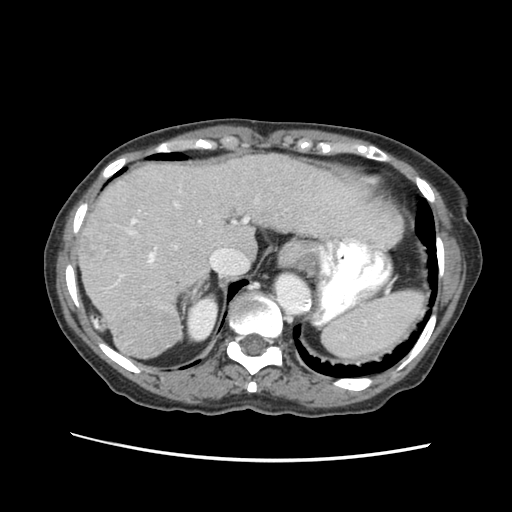
Contrast-enhanced abdominal CT (liver protocol), one axial slice. Slice 44 of 63 in the series (ordered by position). Reconstruction kernel STANDARD. Soft-tissue window (W 400 / L 40 HU). 512 × 512 image matrix, field of view 340 × 340 mm. Case-level facts recorded for this patient, not image findings: diagnosis: hepatocellular carcinoma (patient treated with transarterial chemoembolisation; whether this scan precedes or follows treatment is not stated here); TNM stage (as recorded): Stage-I; Child-Pugh class: B; tumour differentiation: well differentiated.
Outlined on this slice (semi-automatically segmented with operator editing):
- liver parenchyma outside the tumour (the mass and vessels are separate outlines, so this box may not span the whole liver): bounding box [x1, y1, x2, y2] px = [76, 150, 402, 358]
- mass: [113, 302, 179, 357]
- liver vessels: [130, 187, 248, 265]